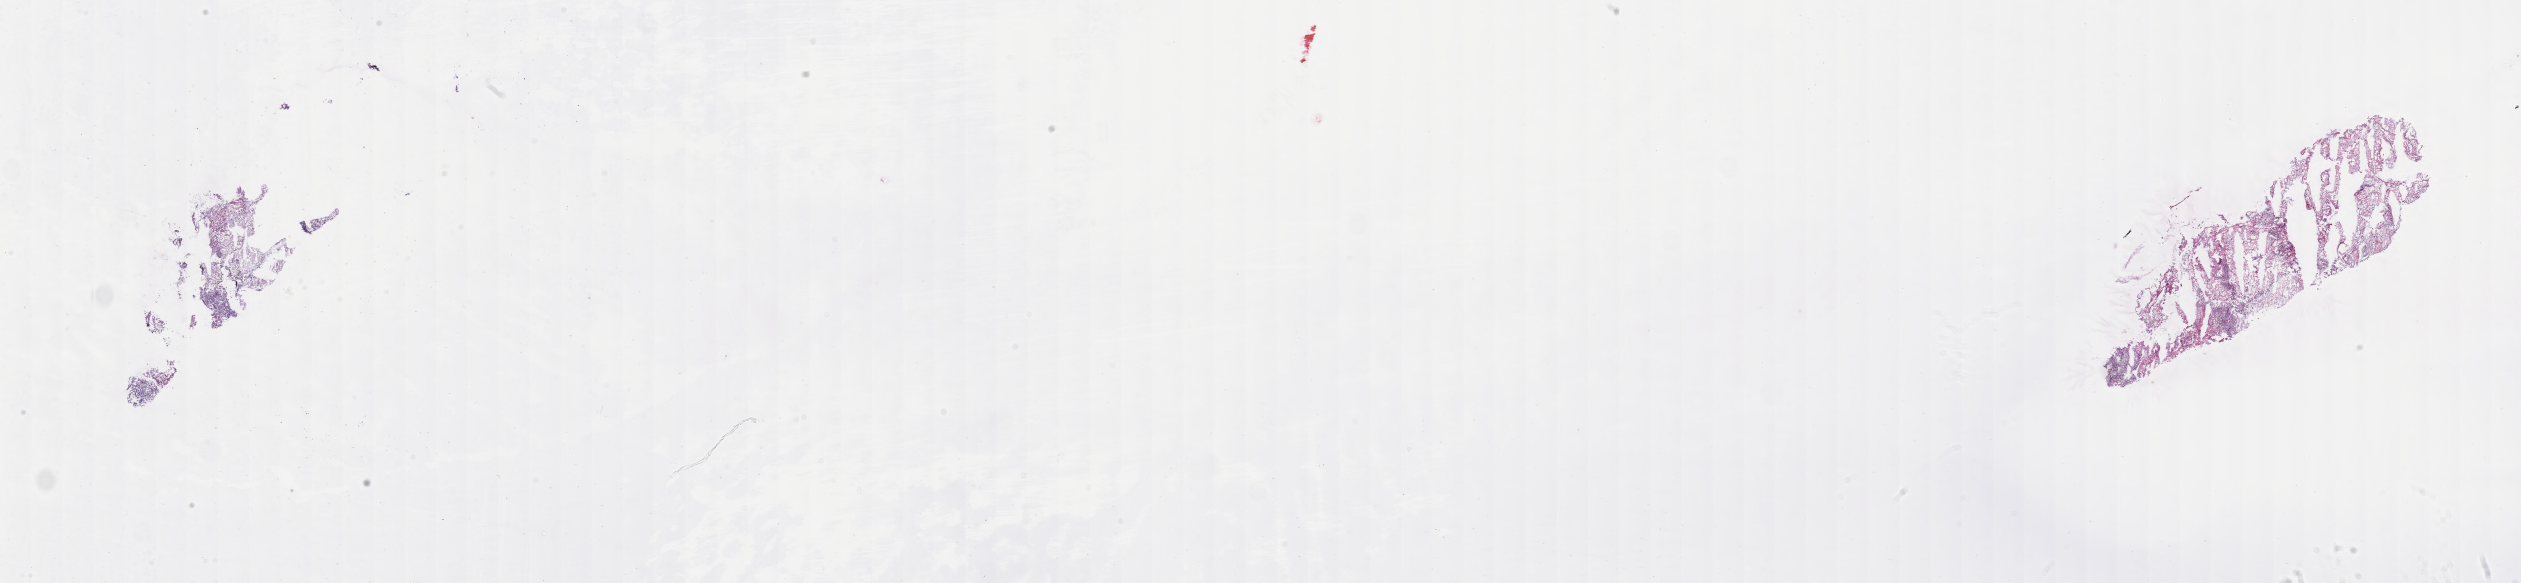
Hematoxylin and eosin (H&E) whole-slide image of tumor tissue from the brain — low-resolution overview of the scanned area, about 40.8 x 9.4 mm, frozen section (OCT-embedded). Female patient, age 117 months (9 years 9 months).
• recorded diagnosis: Glioma, malignant